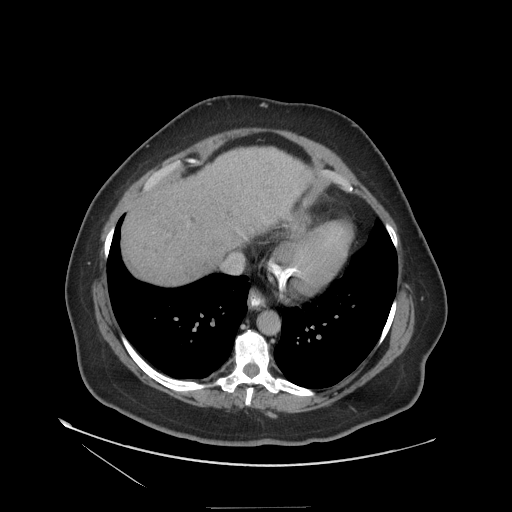
Contrast-enhanced abdominal CT (liver protocol), one axial slice. Position 103 of 127 along the scan axis. Reconstruction kernel STANDARD. 140 kVp. Soft-tissue window (W 400 / L 40 HU). 2.5 mm slice thickness. 512 × 512 image matrix, field of view 480 × 480 mm. Case-level facts recorded for this patient, not image findings: diagnosis: hepatocellular carcinoma (patient treated with transarterial chemoembolisation; whether this scan precedes or follows treatment is not stated here); TNM stage (as recorded): Stage-II; Child-Pugh class: A.
Outlined on this slice (semi-automatic segmentation, software-assisted and operator-edited):
- liver parenchyma outside the tumour (the mass and vessels are separate outlines, so this box may not span the whole liver): bounding box <122,148,312,284> (left, top, right, bottom; pixels)
- liver vessels: <146,179,155,189>